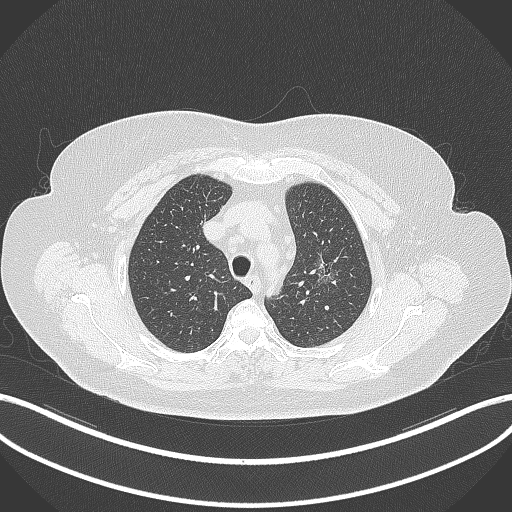
Chest CT, one axial slice. Slice 266 of 309 in the series (ordered by position). Reconstruction kernel B70f. Lung window (W 1500 / L -600 HU). 512 × 512 image matrix, field of view 400 × 400 mm. Female patient, age 70 years. From the clinical record (not read from this slice): clinical TNM (as recorded): T1c N0 M0.
Structures marked on this image (rectangle marked by the reading radiologist):
- lung tumour (recorded histology: adenocarcinoma): bounding box [x1, y1, x2, y2] px = [311, 253, 340, 290]